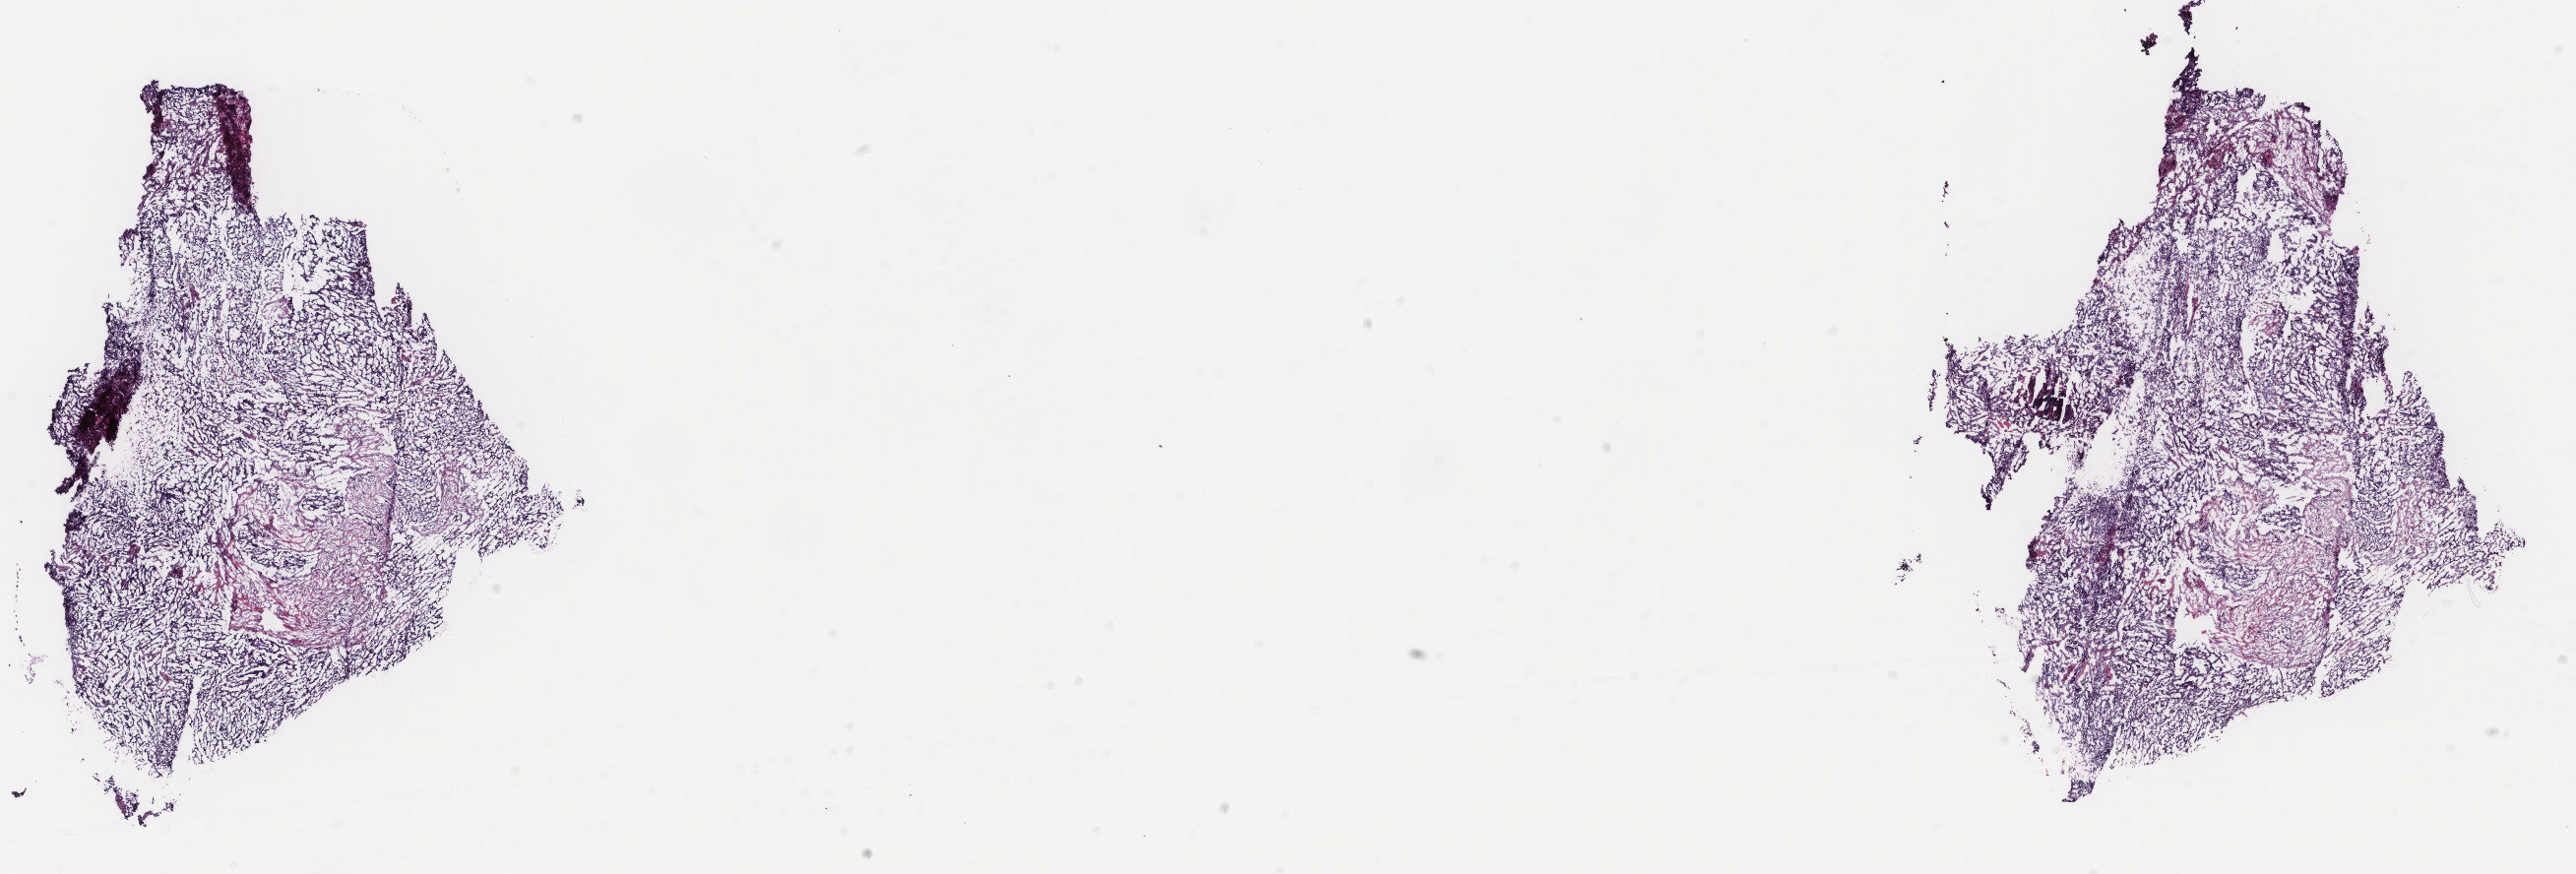
H&E-stained whole-slide image, shown as a low-resolution overview of the whole scanned area (about 20.8 x 7.0 mm, slide scanned at 40x). Frozen section from the top of the tissue portion. Sample: primary tumour, uterus. Female patient; age at initial diagnosis 69 years. Histologic grade: G3 (poorly differentiated). Pathologist review of this section (percent, as recorded): tumour cells 73%, tumour nuclei 75%, normal cells 20%, stromal cells 5%, necrosis 2%. Infiltration values recorded for this section: lymphocyte infiltration 1%, monocyte infiltration 0%, neutrophil infiltration 0%.
- FIGO stage: IVB
- diagnosis: Endometrioid adenocarcinoma, NOS (endometrium)